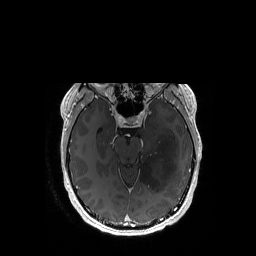
Brain MRI from a brain-tumour surgery series, one axial slice; position 109 of 192 along the scan axis; T1-weighted post-contrast; 1 mm slice thickness; 256 × 256 image matrix. Case-level facts recorded for this patient, not image findings: histopathology: Astrocytoma; WHO grade: 3; IDH mutation: yes; tumour location: Left Temporal.
Annotated regions visible in this slice (manually delineated by an expert):
- tumour: bounding box (x1, y1, x2, y2) in pixels: (139, 132, 178, 191)